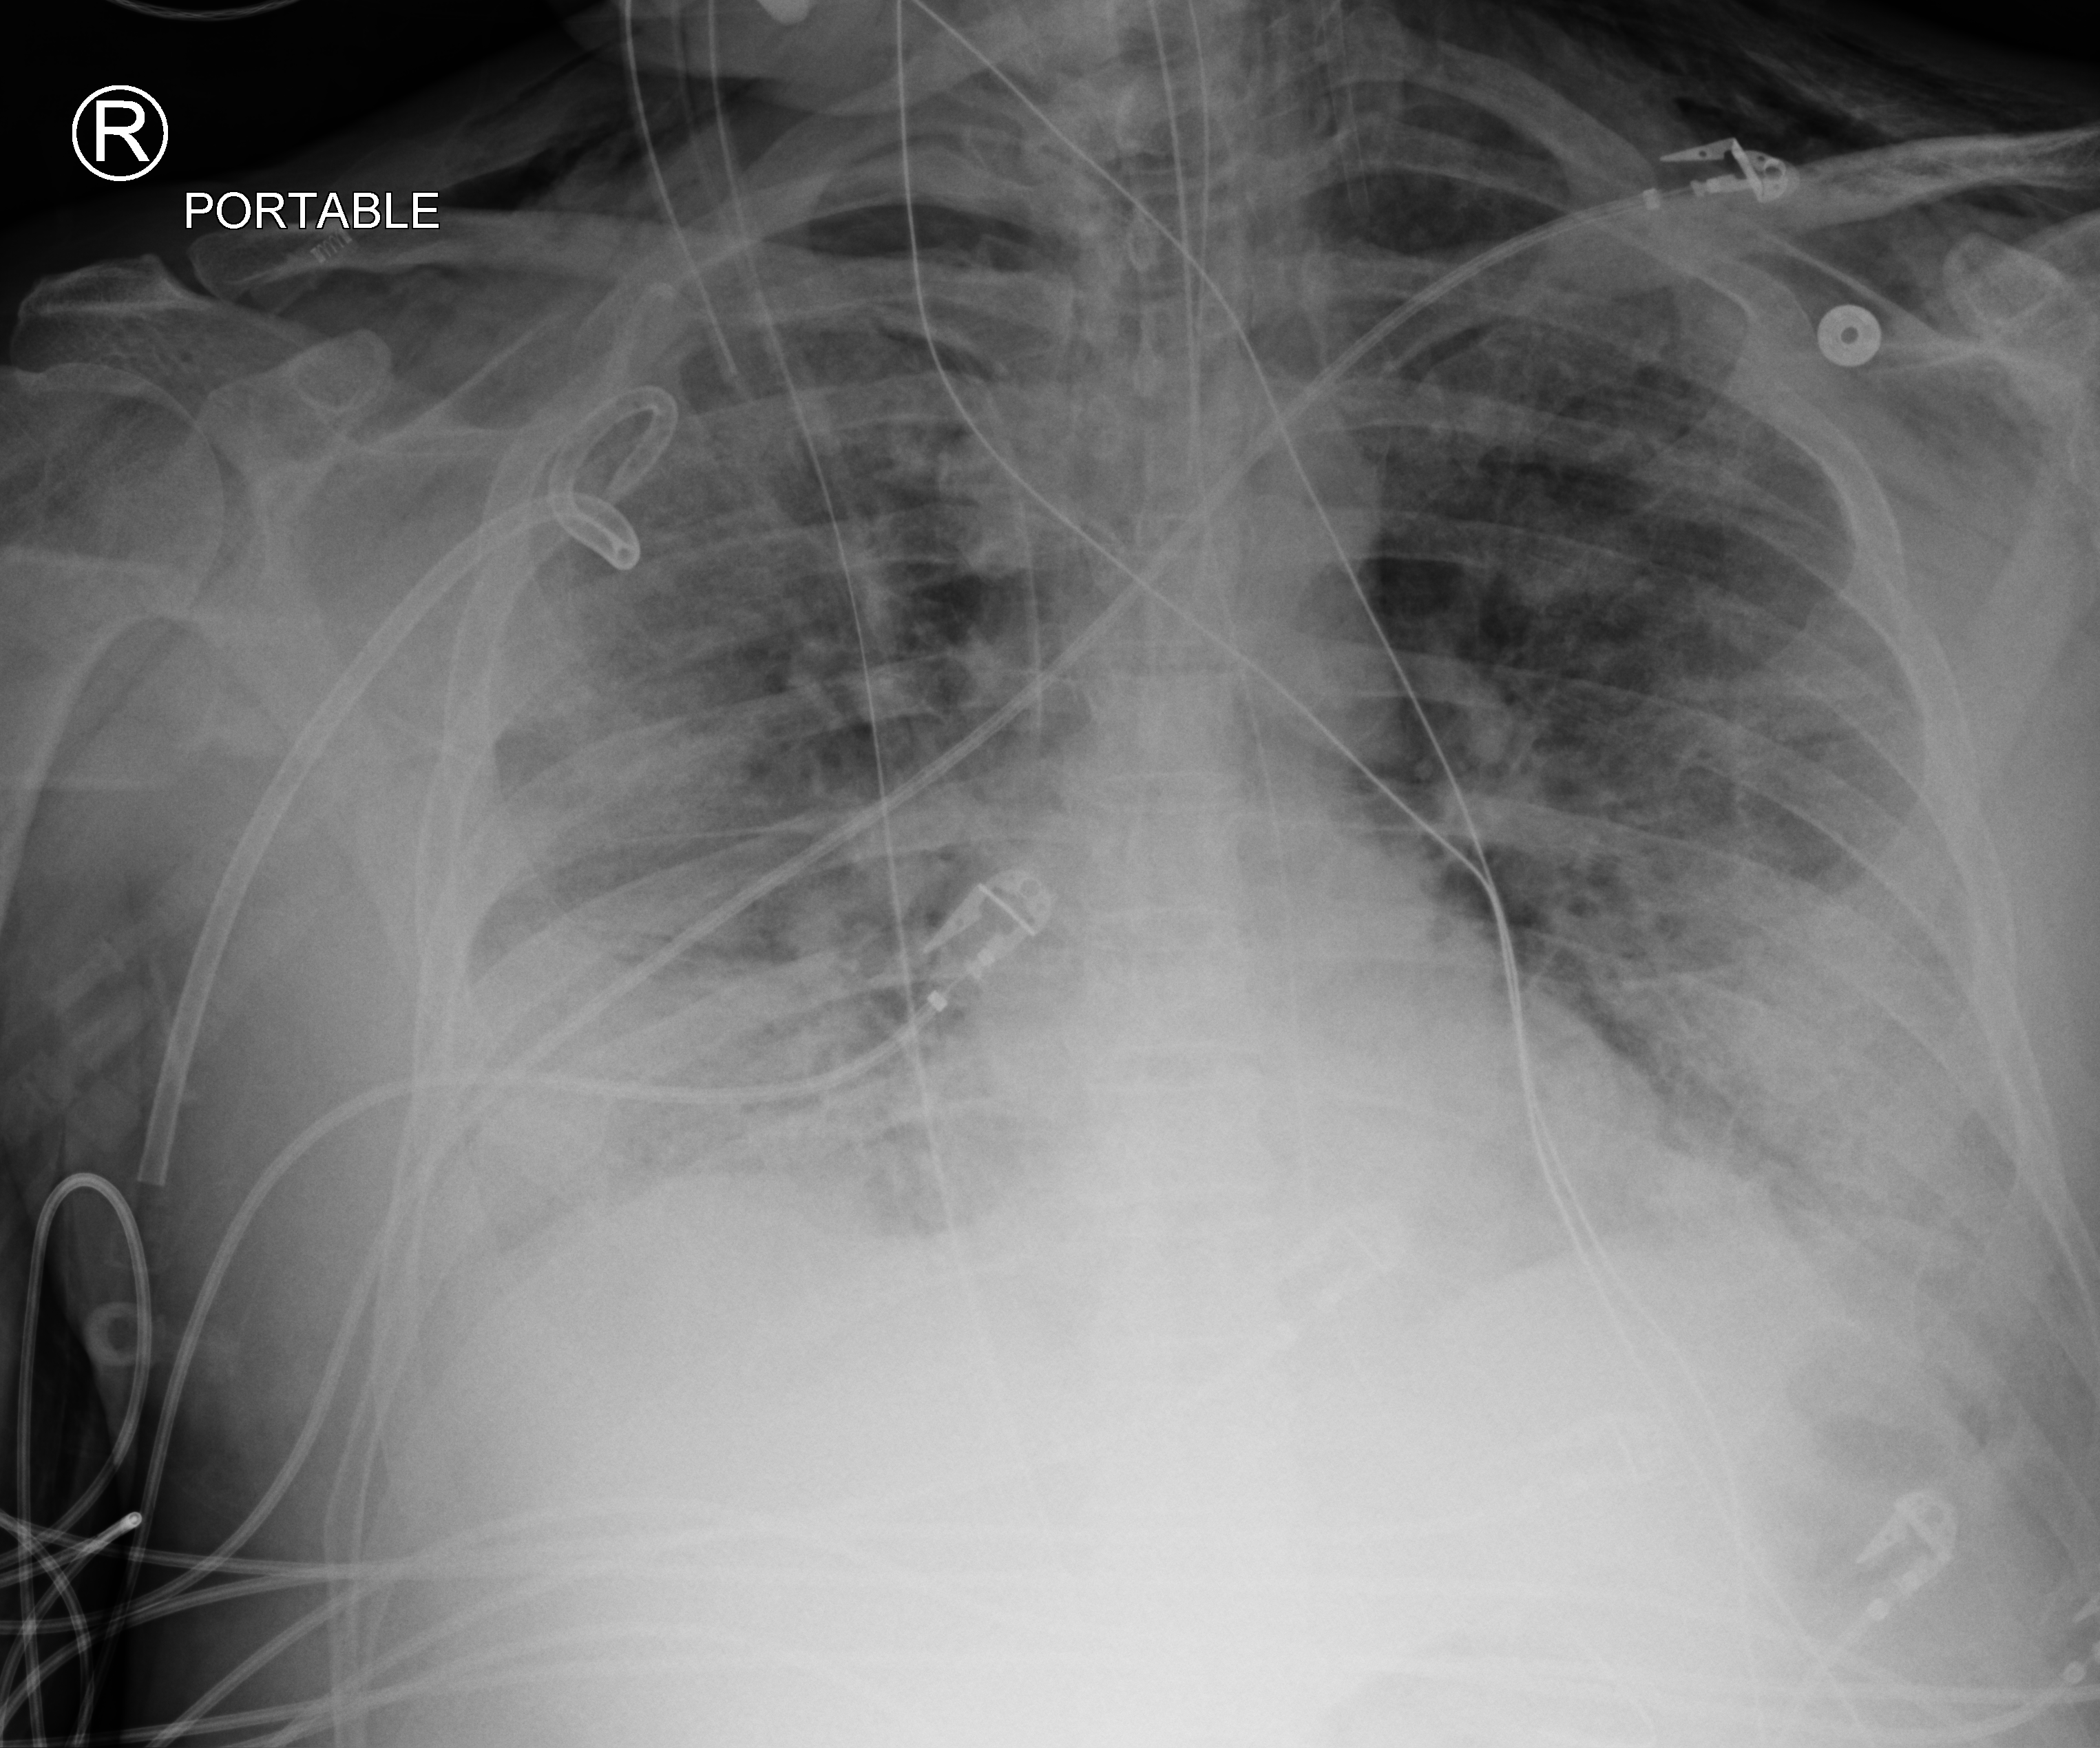
Portable chest radiograph, anteroposterior (AP) projection. Patient hospitalised with COVID-19; male, aged 60–74 years.
Hospital-stay facts (about this admission, not read from this image; timing relative to this image not recorded): mechanically ventilated during this hospital stay: yes; admitted to intensive care during this hospital stay: yes; COPD (admission record): no.